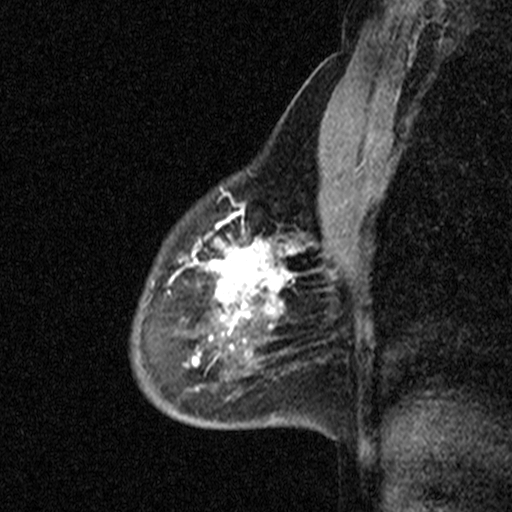
Breast MRI (dynamic contrast-enhanced), one sagittal slice. Slice 31 of 44 in the series (ordered by position). Dynamic contrast-enhanced study with each time point stored as its own series, time point 2 of 3 at this slice position (early post-contrast, ordered by acquisition time). 1.5 T. TE 4.5 ms, TR 11 ms. 3 mm slice thickness. 512 × 512 image matrix. Female patient, age 53 years. From the clinical record (not read from this slice): setting: breast cancer imaged before/during neoadjuvant chemotherapy; receptor status: HR-positive, HER2-negative.
Outlined on this slice (semi-automatic segmentation, software-assisted and operator-edited):
- analysis volume of interest (the breast-tissue region the enhancement analysis was run in; not a lesion): box from (x=88, y=176) to (x=313, y=423) px
- tumour enhancement mask (voxels above the 90 % enhancement threshold inside the analysis volume of interest): (x=169, y=197)–(x=304, y=354)